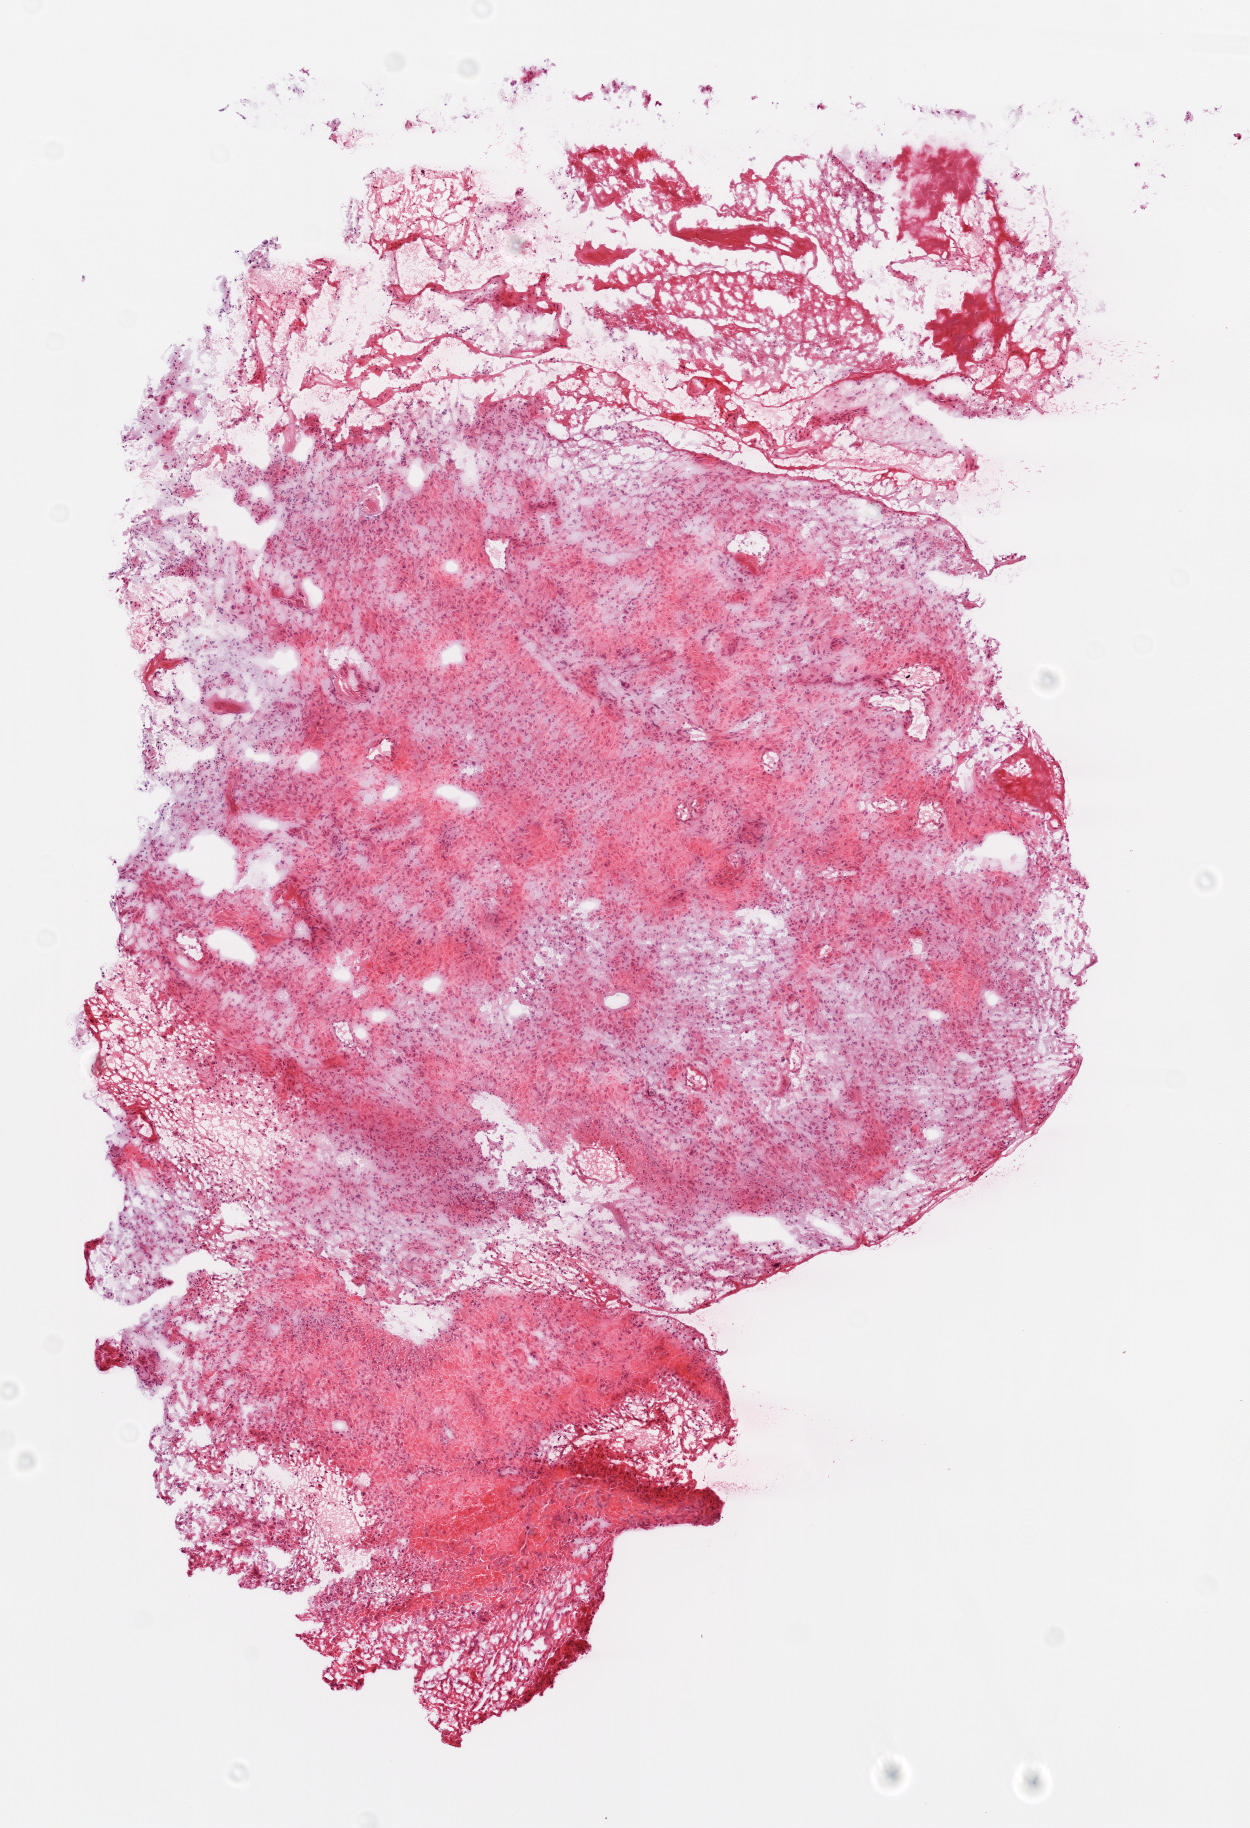
H&E-stained whole-slide image, whole scanned area (about 5.0 x 7.3 mm, slide scanned at 20x) shown as a low-resolution overview. Frozen section from the top of the tissue portion. Sample: primary tumour, brain. Male patient; age at initial diagnosis 57 years. Pathologist review of this section (percent, as recorded): tumour cells 70%, tumour nuclei 85%, normal cells 0%, stromal cells 15%, necrosis 15%.
Pathologic diagnosis: Glioblastoma.